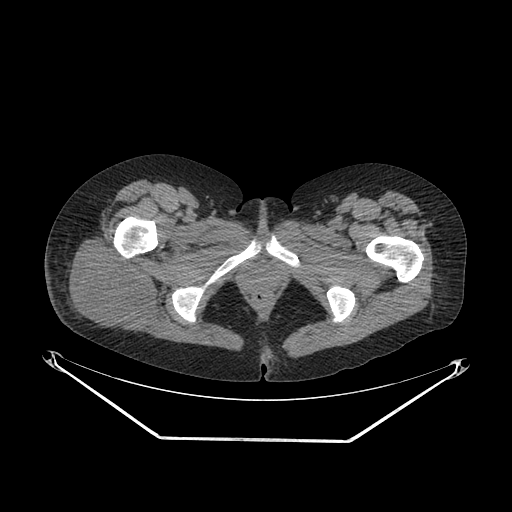
CT of an extremity soft-tissue mass (from a PET/CT study), one axial slice. Slice 38 of 267 in the series (ordered by position). Reconstruction kernel SOFT. Soft-tissue window (W 400 / L 40 HU). 512 × 512 image matrix, field of view 500 × 500 mm. Female patient. From the clinical record (not read from this slice): histological type: epithelioid sarcoma with vascular differentiation; site of the primary tumour: right buttock.
Annotated regions visible in this slice (expert contour drawn on MRI and transferred to this co-registered scan by the dataset authors):
- gross tumour volume (mass): bounding box (x1, y1, x2, y2) in pixels: (66, 235, 156, 330)